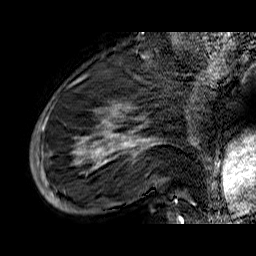
Breast MRI (dynamic contrast-enhanced), one sagittal slice. Position 17 of 60 along the scan axis. Dynamic contrast-enhanced series, time point 2 of 6 at this slice position (early post-contrast). 1.5 T. TE 6.5 ms, TR 32.9 ms. 256 × 256 image matrix, field of view 200 × 200 mm. Female patient. Case-level facts recorded for this patient, not image findings: setting: breast cancer imaged before/during neoadjuvant chemotherapy; receptor status: HR-positive, HER2-negative.
Outlined on this slice (semi-automatic segmentation, software-assisted and operator-edited):
- analysis volume of interest (the breast-tissue region the enhancement analysis was run in; not a lesion): bounding box <33,74,176,210> (left, top, right, bottom; pixels)
- tumour enhancement mask (voxels above the 100 % enhancement threshold inside the analysis volume of interest): <35,106,176,203>